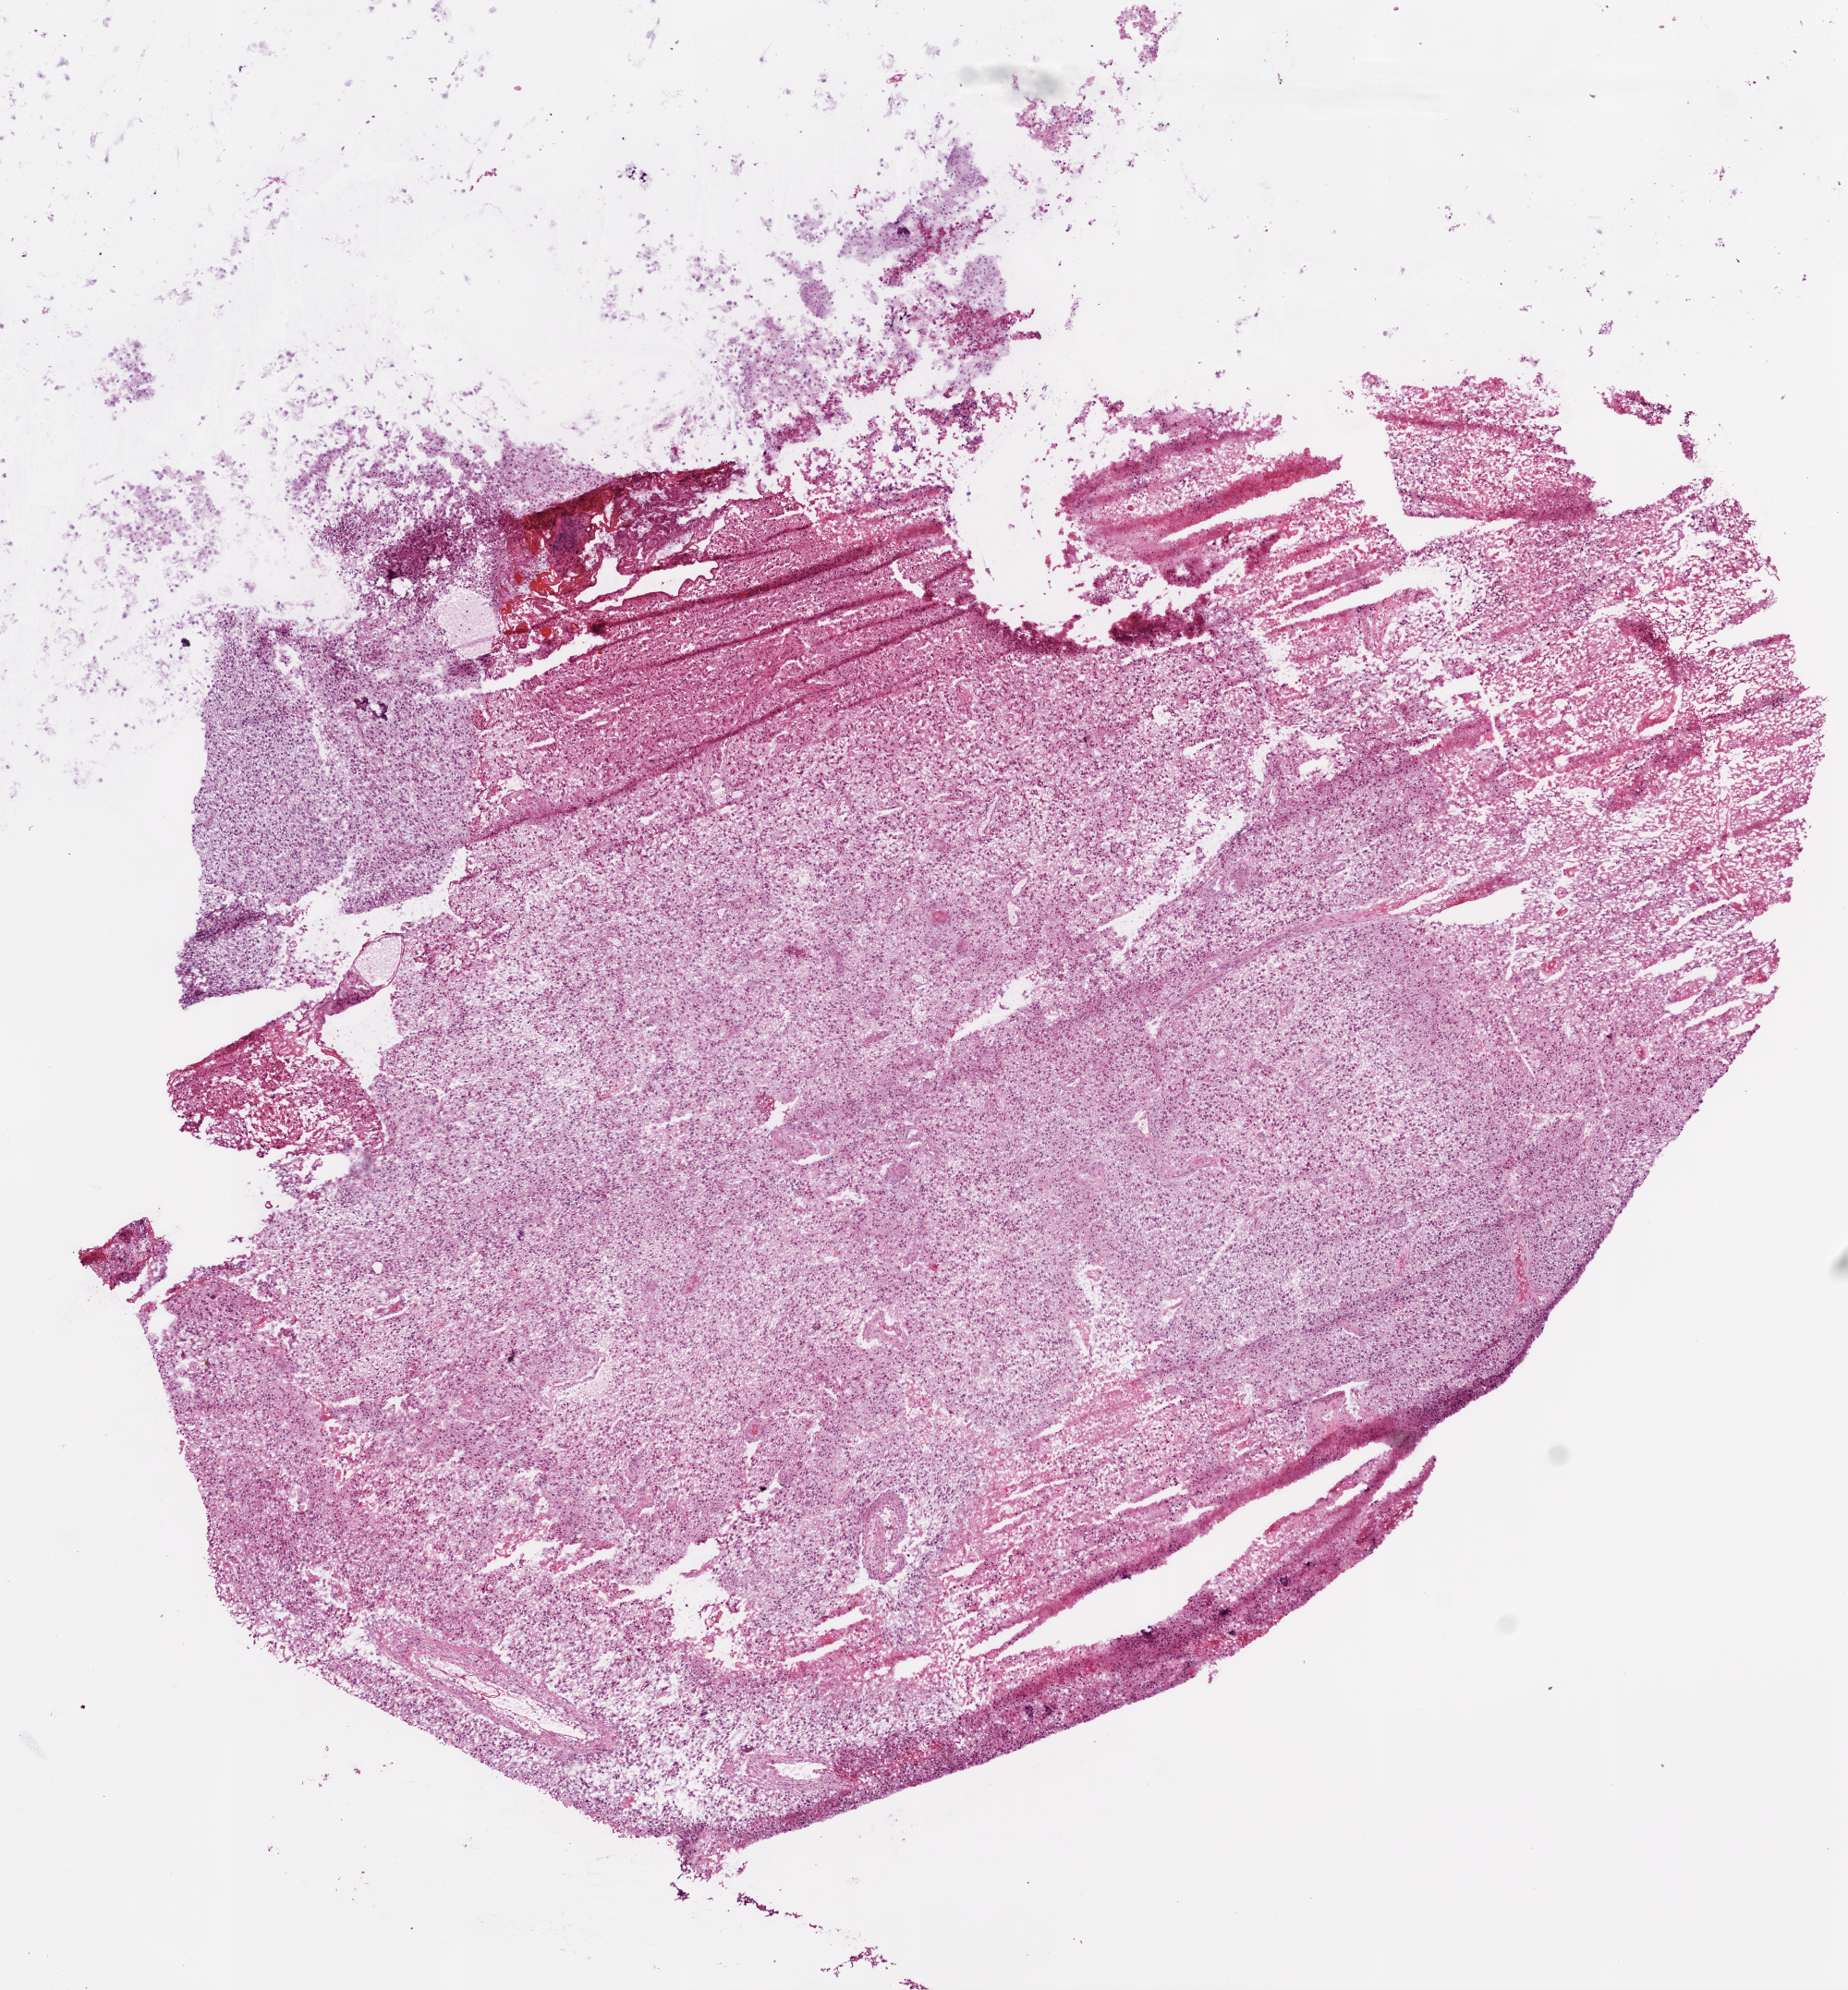
H&E-stained whole-slide image, low-resolution overview of the scanned area, about 8.0 x 8.6 mm (slide scanned at 20x); frozen section from the bottom of the tissue portion; primary tumour sample from the brain. Patient: male, age at initial diagnosis 62 years. Composition of this section per pathologist review: tumour cells 85%, tumour nuclei 85%, normal cells 0%, stromal cells 0%, necrosis 15%.
Histologic diagnosis: Glioblastoma.